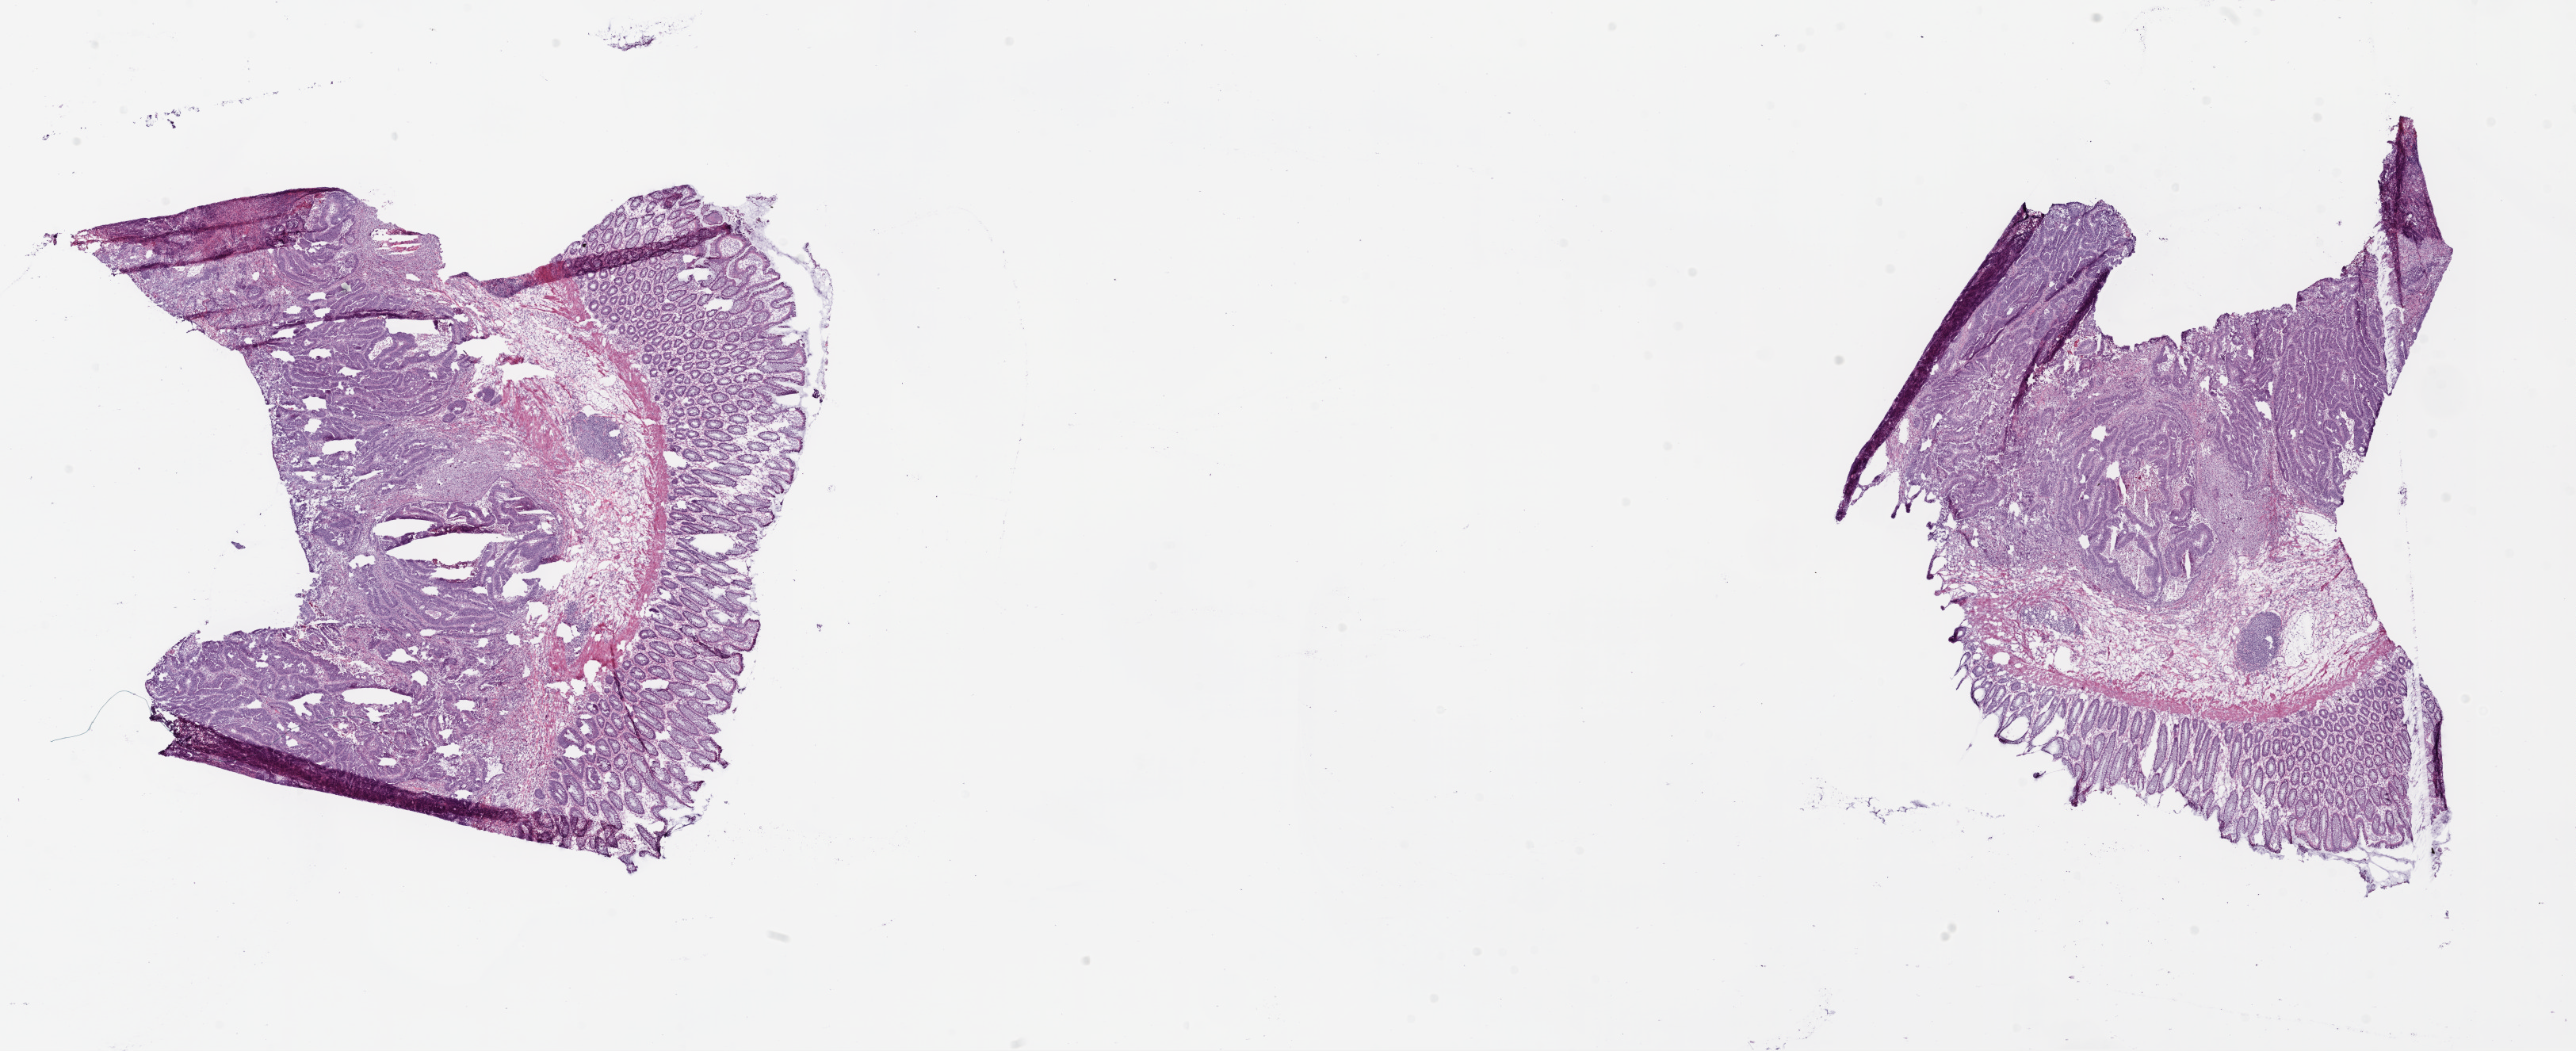
Whole-slide histology image, H&E, whole scanned area (about 26.1 x 10.6 mm, slide scanned at 20x) shown as a low-resolution overview. Frozen section from the bottom of the tissue portion. Sample: primary tumour, rectum. Female patient; age at initial diagnosis 66 years. Slide review estimates, as recorded: tumour cells 55%, tumour nuclei 65%, normal cells 20%, stromal cells 20%, necrosis 5%.
* lymph nodes positive (case pathology): 0 of 13 examined
* diagnosis: Adenocarcinoma, NOS
* AJCC pathologic stage: I (6th edition)